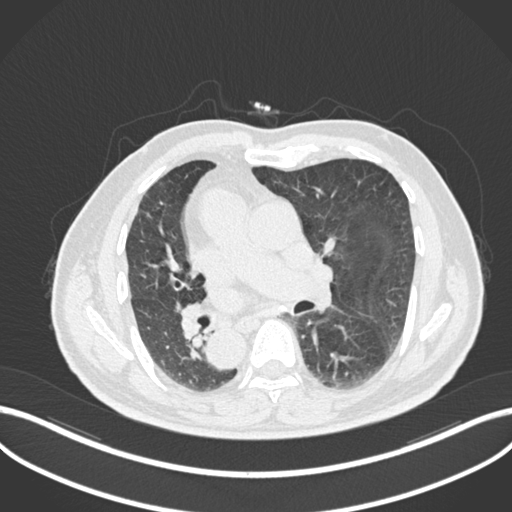
Chest CT, one axial slice; position 116 of 206 along the scan axis; reconstruction kernel B30f; lung window (W 1500 / L -600 HU); 1 mm slice thickness; 512 × 512 image matrix. Male patient, age 67 years. From the clinical record (not read from this slice): clinical TNM (as recorded): T2a N0 M0.
Outlined on this slice (bounding box drawn by a radiologist):
- lung tumour (recorded histology: squamous cell carcinoma): box from (x=176, y=301) to (x=211, y=343) px